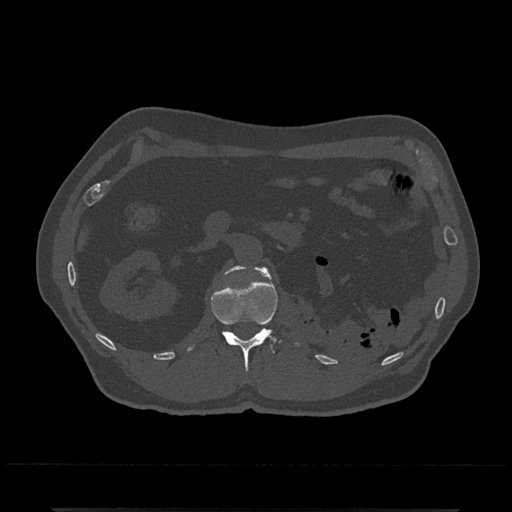
CT including the spine, one axial slice; slice 352 of 797 in the series (ordered by position); reconstruction kernel Br40s/3; 120 kVp; bone window (W 1800 / L 400 HU); 0.5 mm slice thickness; 512 × 512 image matrix. Male patient, age 67 years. Case-level facts recorded for this patient, not image findings: primary cancer: prostate.
Outlined on this slice (semi-automatically segmented with operator editing):
- L1 vertebra: bounding box <188,266,299,372> (left, top, right, bottom; pixels)